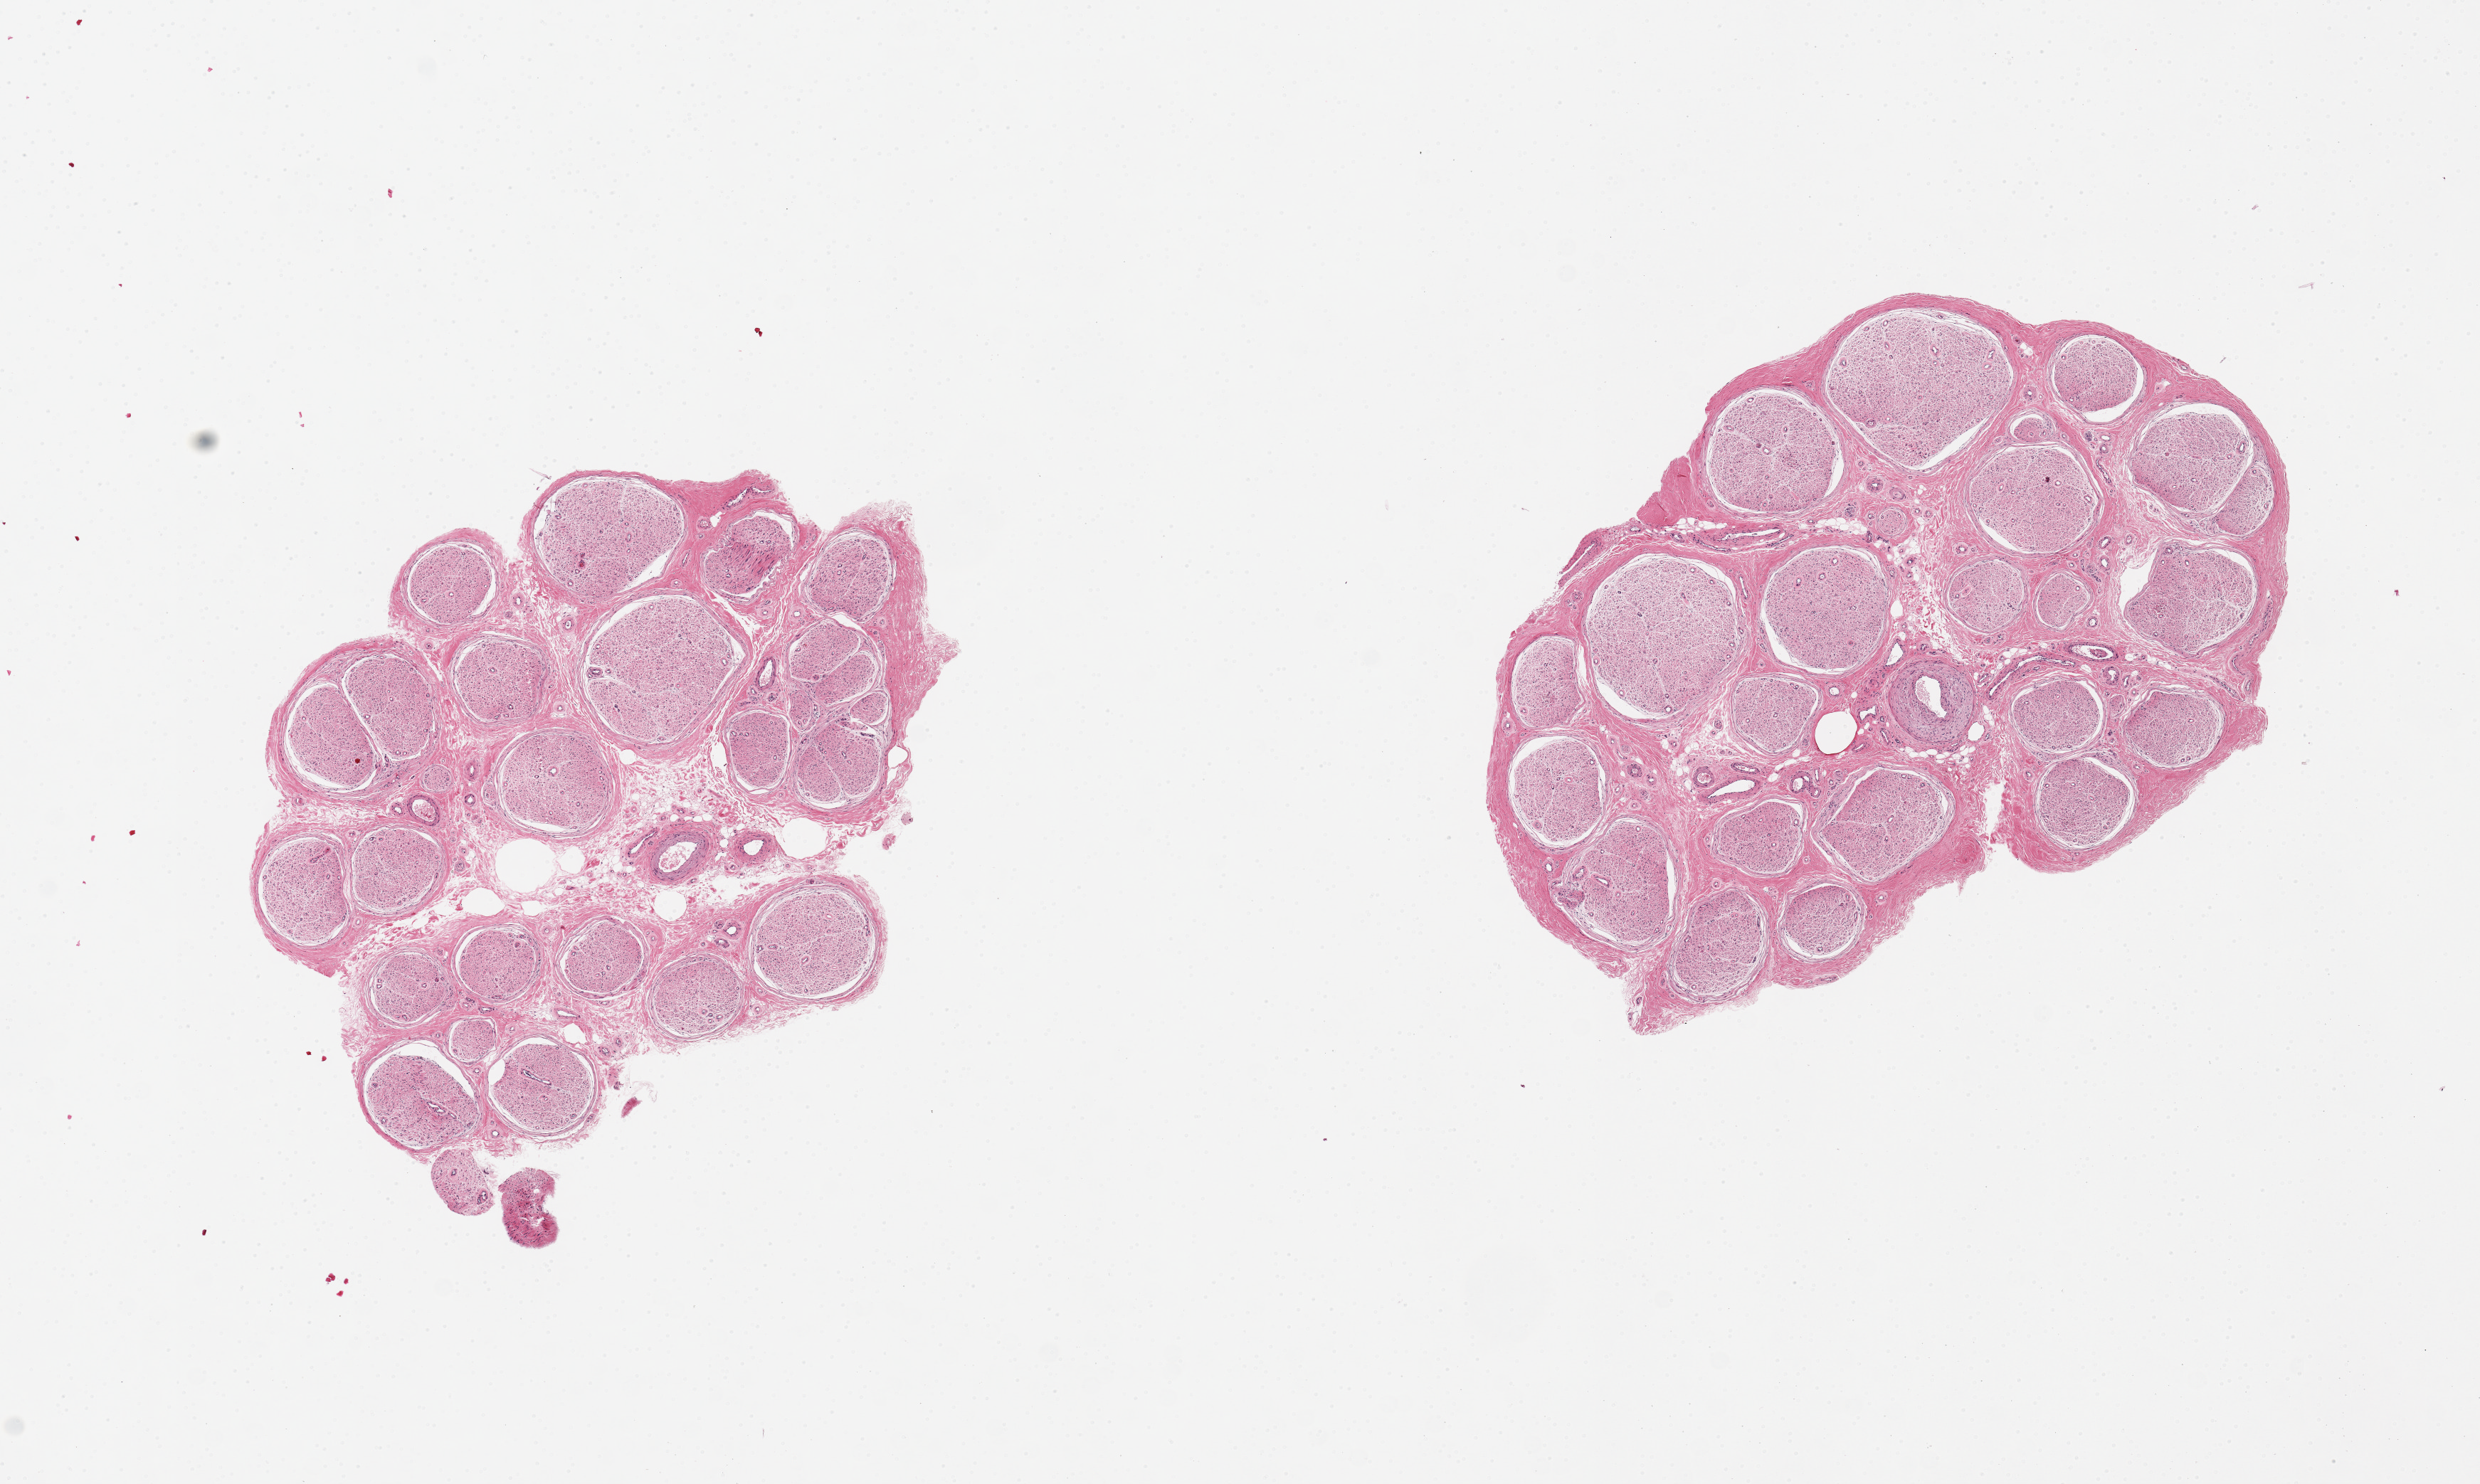
Whole-slide image, haematoxylin and eosin stain, brightfield — whole scanned area (about 13.8 x 8.2 mm) shown as a low-resolution overview, PAXgene-fixed paraffin-embedded (PFPE) section, target tissue: tibial nerve, donor tissue sample. Donor sex: male.
Reviewer comment on this tissue sample: 2 pieces; well-trimmed.